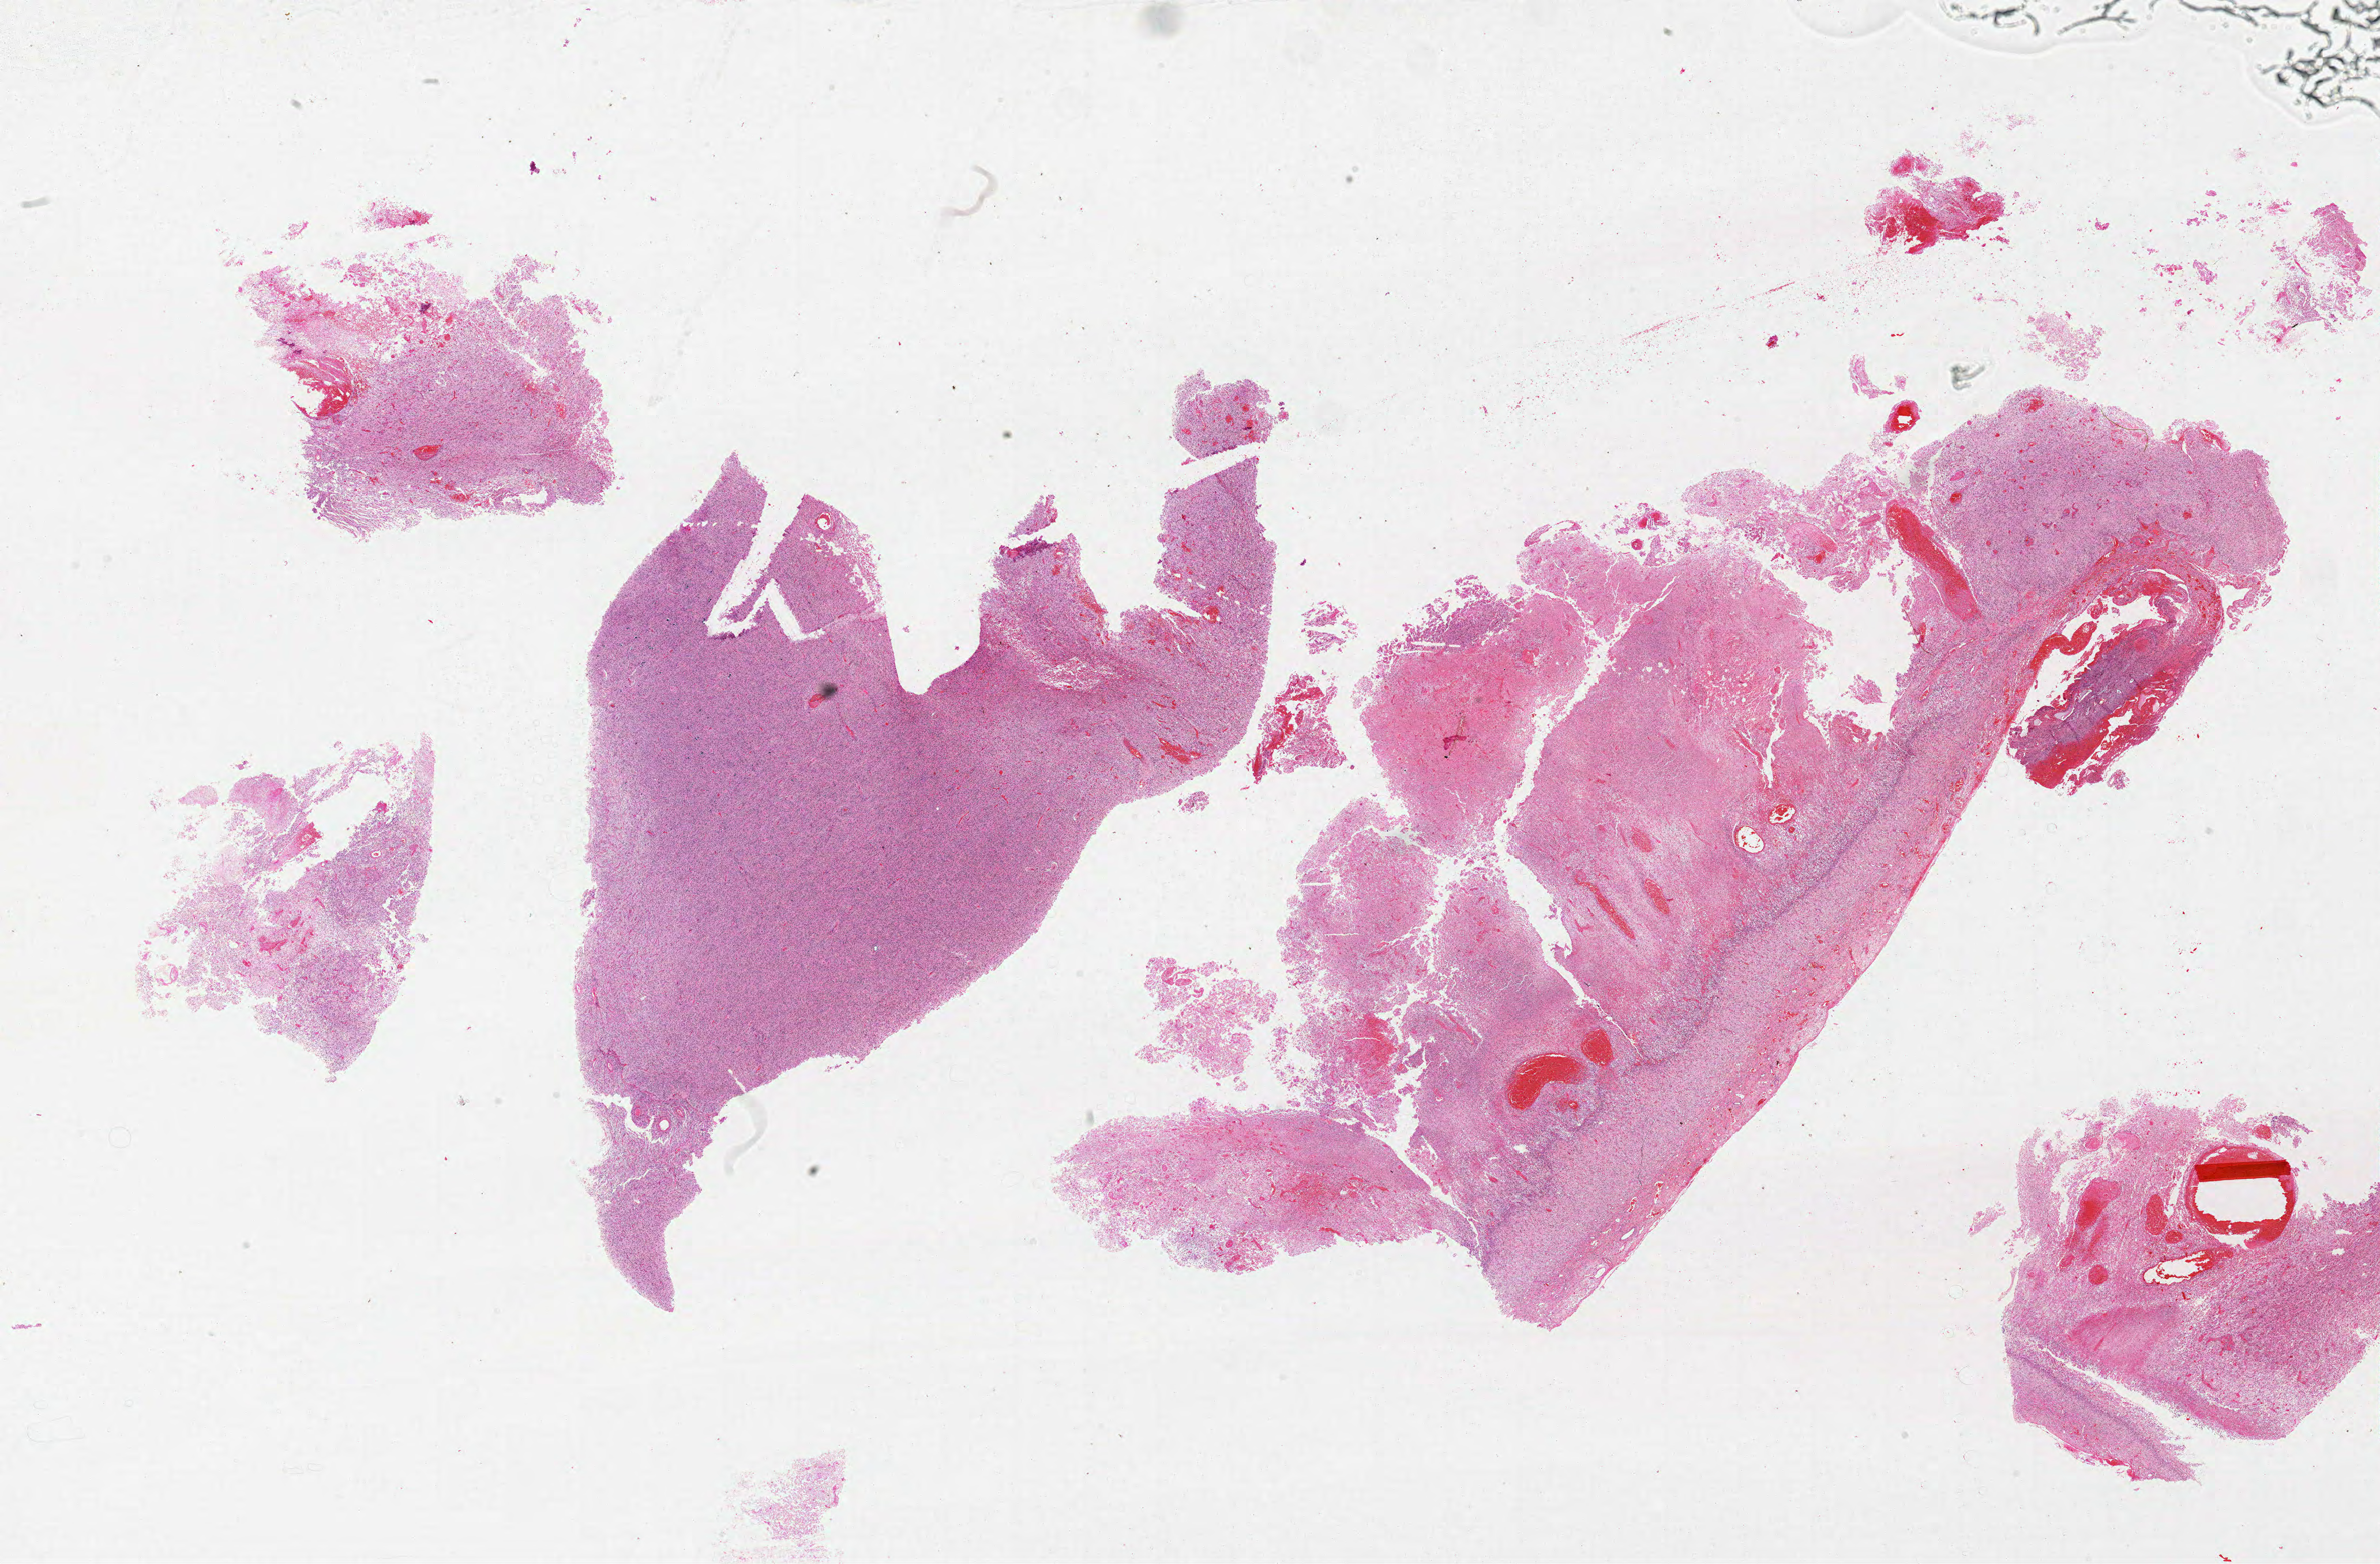
Digitized H&E tissue section (whole slide), low-resolution overview of the scanned area, about 33.0 x 21.7 mm (from a 20x scan). Formalin-fixed paraffin-embedded (FFPE) diagnostic section. Primary tumour sample from the brain. Female patient; age at initial diagnosis 48 years.
- histologic diagnosis: Glioblastoma